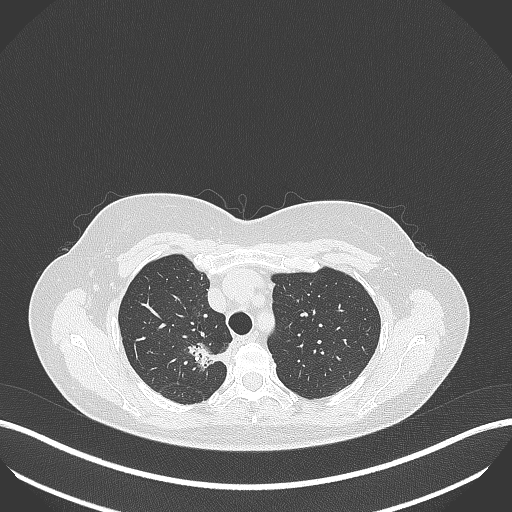
Chest CT, one axial slice. Slice 304 of 386 in the series (ordered by position). Reconstruction kernel B70f. 120 kVp. Lung window (W 1500 / L -600 HU). 512 × 512 image matrix, field of view 400 × 400 mm. Female patient, age 65 years. From the clinical record (not read from this slice): clinical TNM (as recorded): T1b N0 M0; histopathological grade: G2.
Outlined on this slice (bounding box drawn by a radiologist):
- lung tumour (recorded histology: adenocarcinoma): box from (x=183, y=336) to (x=230, y=371) px